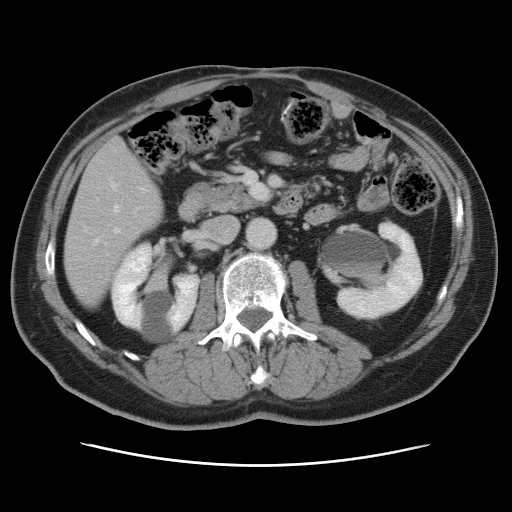
Contrast-enhanced abdominal CT, one axial slice; slice 29 of 80 in the series (ordered by position); 120 kVp; intravenous contrast given; soft-tissue window (W 400 / L 40 HU); 5 mm slice thickness; 512 × 512 image matrix, field of view 370 × 370 mm. Male patient, age 69 years. Case-level facts recorded for this patient, not image findings: diagnosis: colorectal cancer liver metastases, imaged before liver resection; multiple liver metastases: no; largest metastasis: 5 cm; disease in both lobes: yes.
Structures marked on this image (expert manual segmentation):
- hepatic veins: bounding box (x1, y1, x2, y2) in pixels: (93, 182, 119, 244)
- liver: (65, 139, 163, 304)
- planned liver remnant (the part of the liver to remain after resection): (65, 216, 139, 305)
- portal vein (with intrahepatic branches): (113, 228, 120, 234)